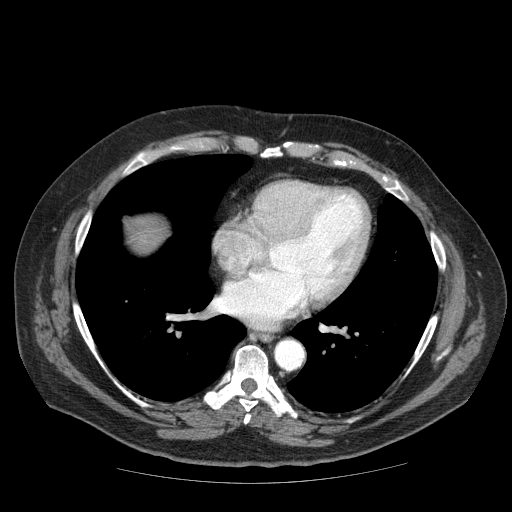
Contrast-enhanced abdominal CT (liver protocol), one axial slice. Position 75 of 85 along the scan axis. Soft-tissue window (W 400 / L 40 HU). 2.5 mm slice thickness. 512 × 512 image matrix, field of view 420 × 420 mm. From the clinical record (not read from this slice): diagnosis: hepatocellular carcinoma (patient treated with transarterial chemoembolisation; whether this scan precedes or follows treatment is not stated here); TNM stage (as recorded): Stage-IIIA; Child-Pugh class: A; tumour nodularity: multinodular.
Annotated regions visible in this slice (semi-automatically segmented with operator editing):
- liver parenchyma outside the tumour (the mass and vessels are separate outlines, so this box may not span the whole liver): bounding box [x1, y1, x2, y2] px = [126, 216, 166, 252]